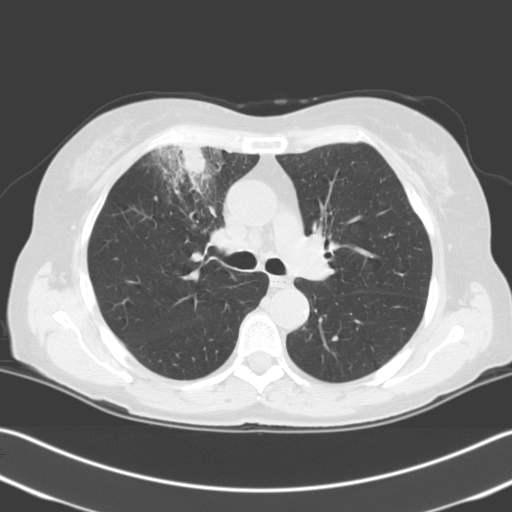
Low-dose screening chest CT, one axial slice; slice 139 of 204 in the series (ordered by position); 140 kVp; lung window (W 1500 / L -600 HU); 3.2 mm slice thickness; 512 × 512 image matrix, field of view 348 × 348 mm.
Annotated regions visible in this slice (expert manual segmentation):
- lesion 1 (tumor, upper lobe of right lung): bounding box <173,143,207,176> (left, top, right, bottom; pixels)